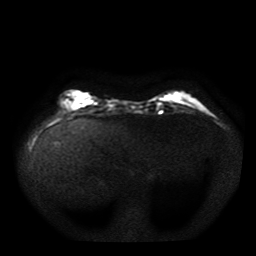
Breast MRI, one axial slice; diffusion-weighted series; image 2 of 4 stored at this slice position (different b-values; order by instance number); 1.5 T; 5 mm slice thickness; 256 × 256 image matrix, field of view 330 × 330 mm. Female patient.
Annotated regions visible in this slice (manually delineated by an expert):
- tumour on diffusion-weighted imaging: bounding box (x1, y1, x2, y2) in pixels: (61, 93, 82, 107)